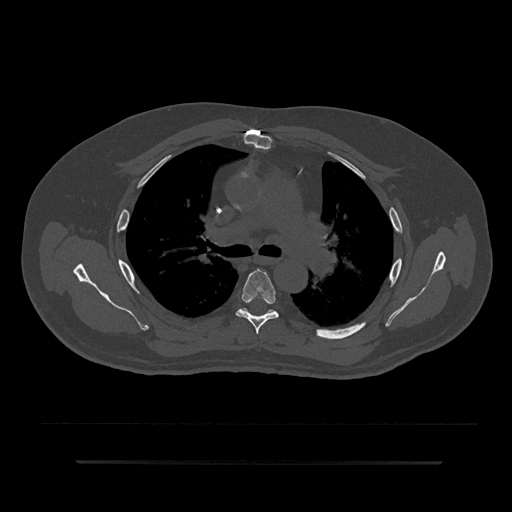
CT including the spine, one axial slice. Position 569 of 797 along the scan axis. Reconstruction kernel Br40s/3. 120 kVp. Bone window (W 1800 / L 400 HU). 512 × 512 image matrix, field of view 464 × 464 mm. Patient: male, 59 years. Case-level facts recorded for this patient, not image findings: primary cancer: bile ducts.
Outlined on this slice (semi-automatically segmented with operator editing):
- T5 vertebra: bounding box [x1, y1, x2, y2] px = [235, 269, 279, 335]
- T6 vertebra: [241, 308, 270, 312]